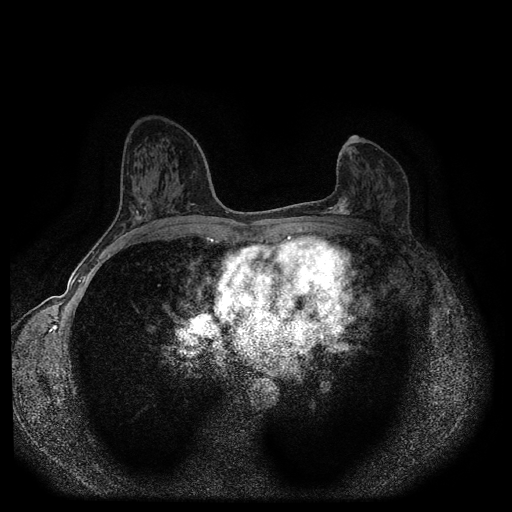
Breast MRI (dynamic contrast-enhanced, multi-phase), one axial slice; position 53 of 116 along the scan axis; dynamic contrast-enhanced series, time point 2 of 5 at this slice position (early post-contrast); 1.5 T; TE 2.6 ms, TR 5.4 ms; 2 mm slice thickness; 512 × 512 image matrix, field of view 340 × 340 mm. Patient: female, 57 years.
Annotated regions visible in this slice (semi-automatically segmented with operator editing):
- breast lesion (labelled 'tumour' in the annotation; benign lesions carry a separate 'benign' label): box from (x=322, y=197) to (x=352, y=217) px